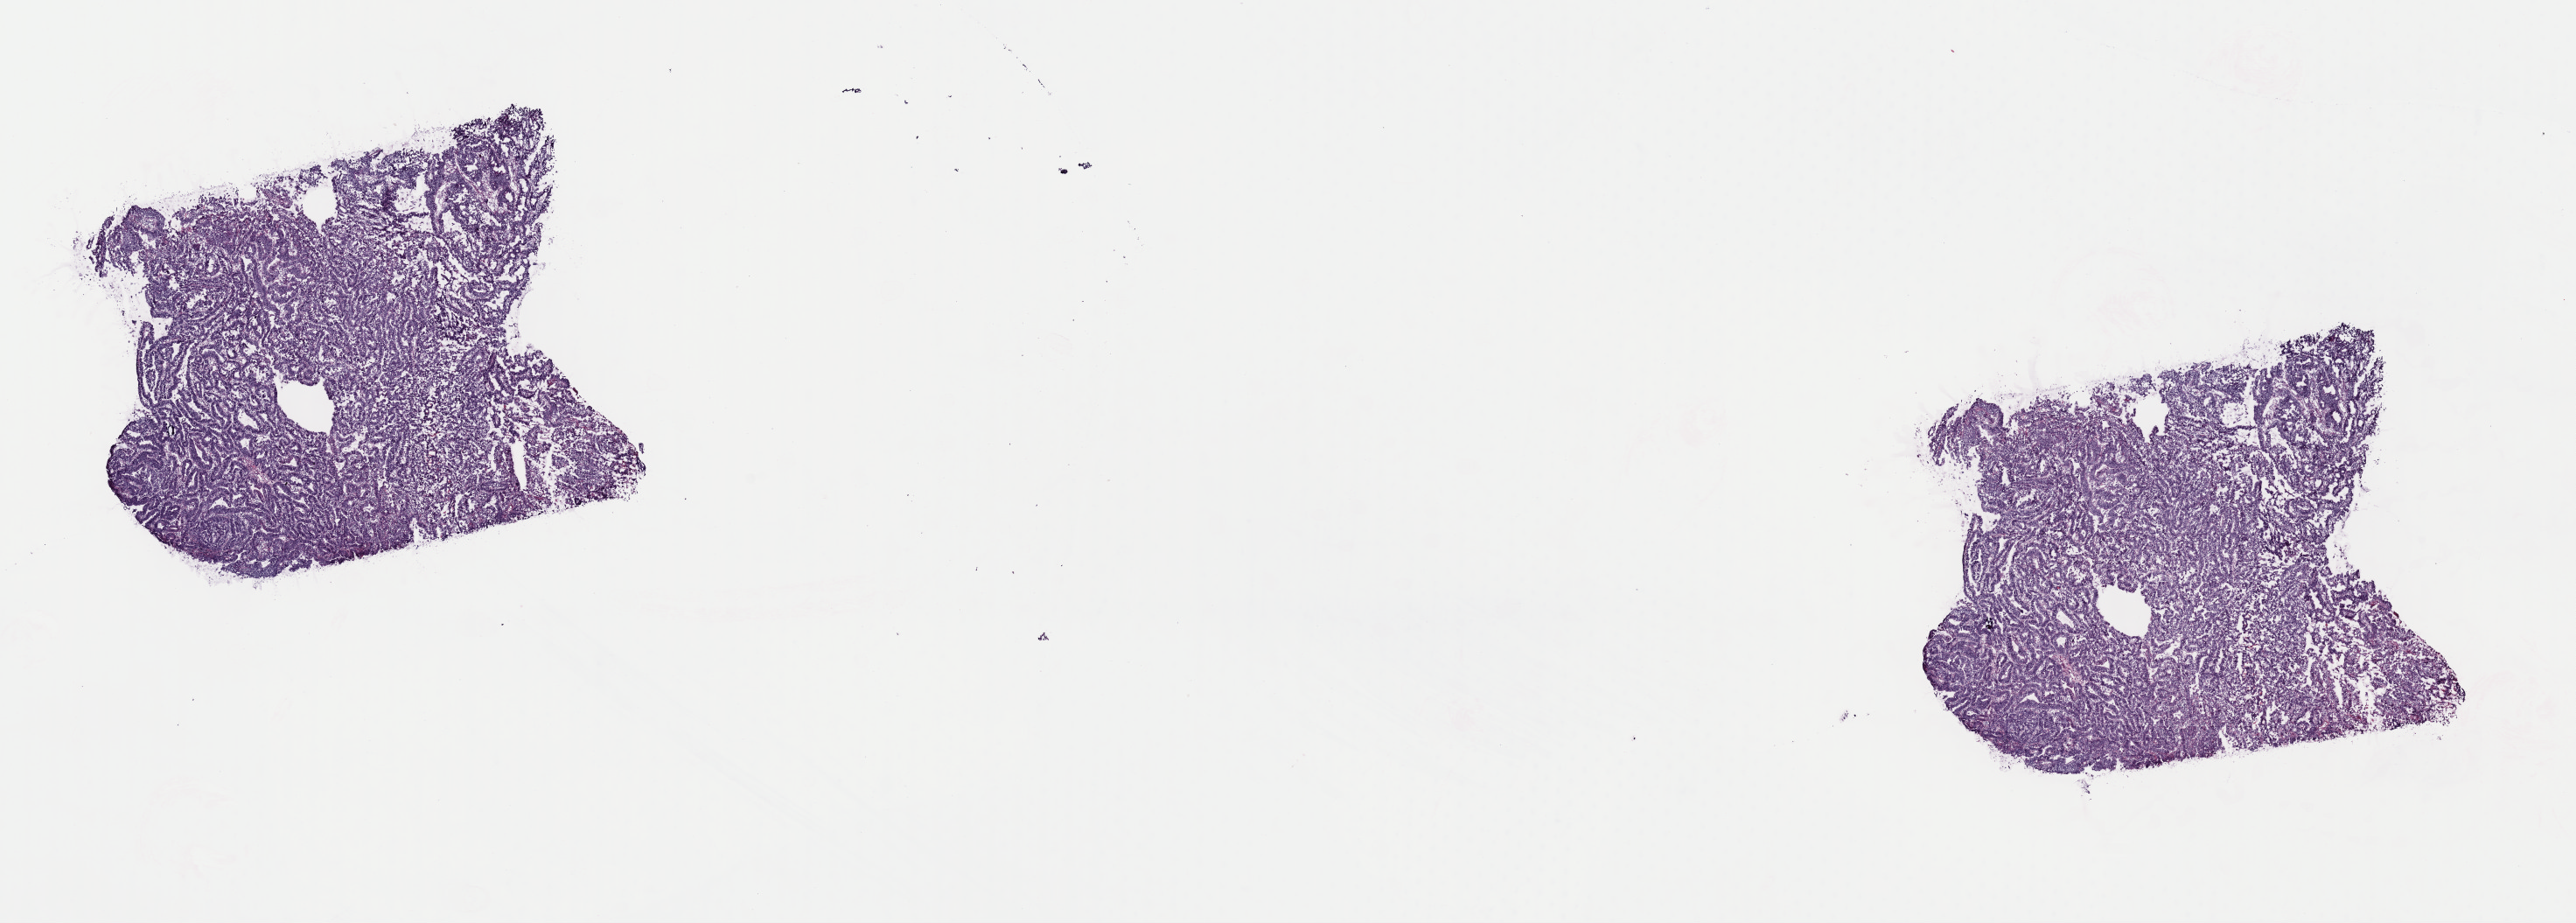
Whole-slide histology image, Hematoxylin and eosin (H&E) stained, whole scanned area (about 23.3 x 8.3 mm) shown as a low-resolution overview; frozen section from the top of the tissue portion; primary tumour sample from the stomach. Patient: male, age at initial diagnosis 56 years. Histologic grade: G3 (poorly differentiated). Composition of this section per pathologist review: tumour cells 80%, tumour nuclei 80%, normal cells 0%, stromal cells 20%, necrosis 0%. Infiltration values recorded for this section: lymphocyte infiltration 4%, monocyte infiltration 2%, neutrophil infiltration 2%.
Diagnosis: Tubular adenocarcinoma (gastric antrum). AJCC pathologic stage: IIB (7th edition).